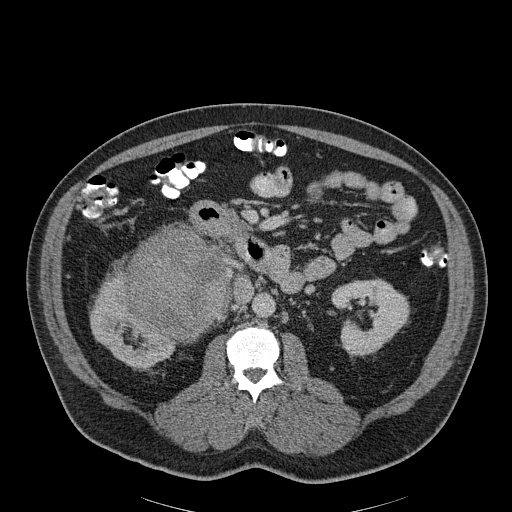
Contrast-enhanced abdominal CT, one axial slice. Position 109 of 186 along the scan axis. 120 kVp. Soft-tissue window (W 400 / L 40 HU). 3 mm slice thickness. 512 × 512 image matrix, field of view 464 × 464 mm. Male patient, age 56 years. From the clinical record (not read from this slice): diagnosis: adrenocortical carcinoma; tumour side: right adrenal; tumour size at pathology: 18 cm; Ki-67 index: 2 %; stage (as recorded): 3.
Annotated regions visible in this slice (semi-automatically segmented with operator editing):
- mass: box from (x=127, y=229) to (x=225, y=338) px